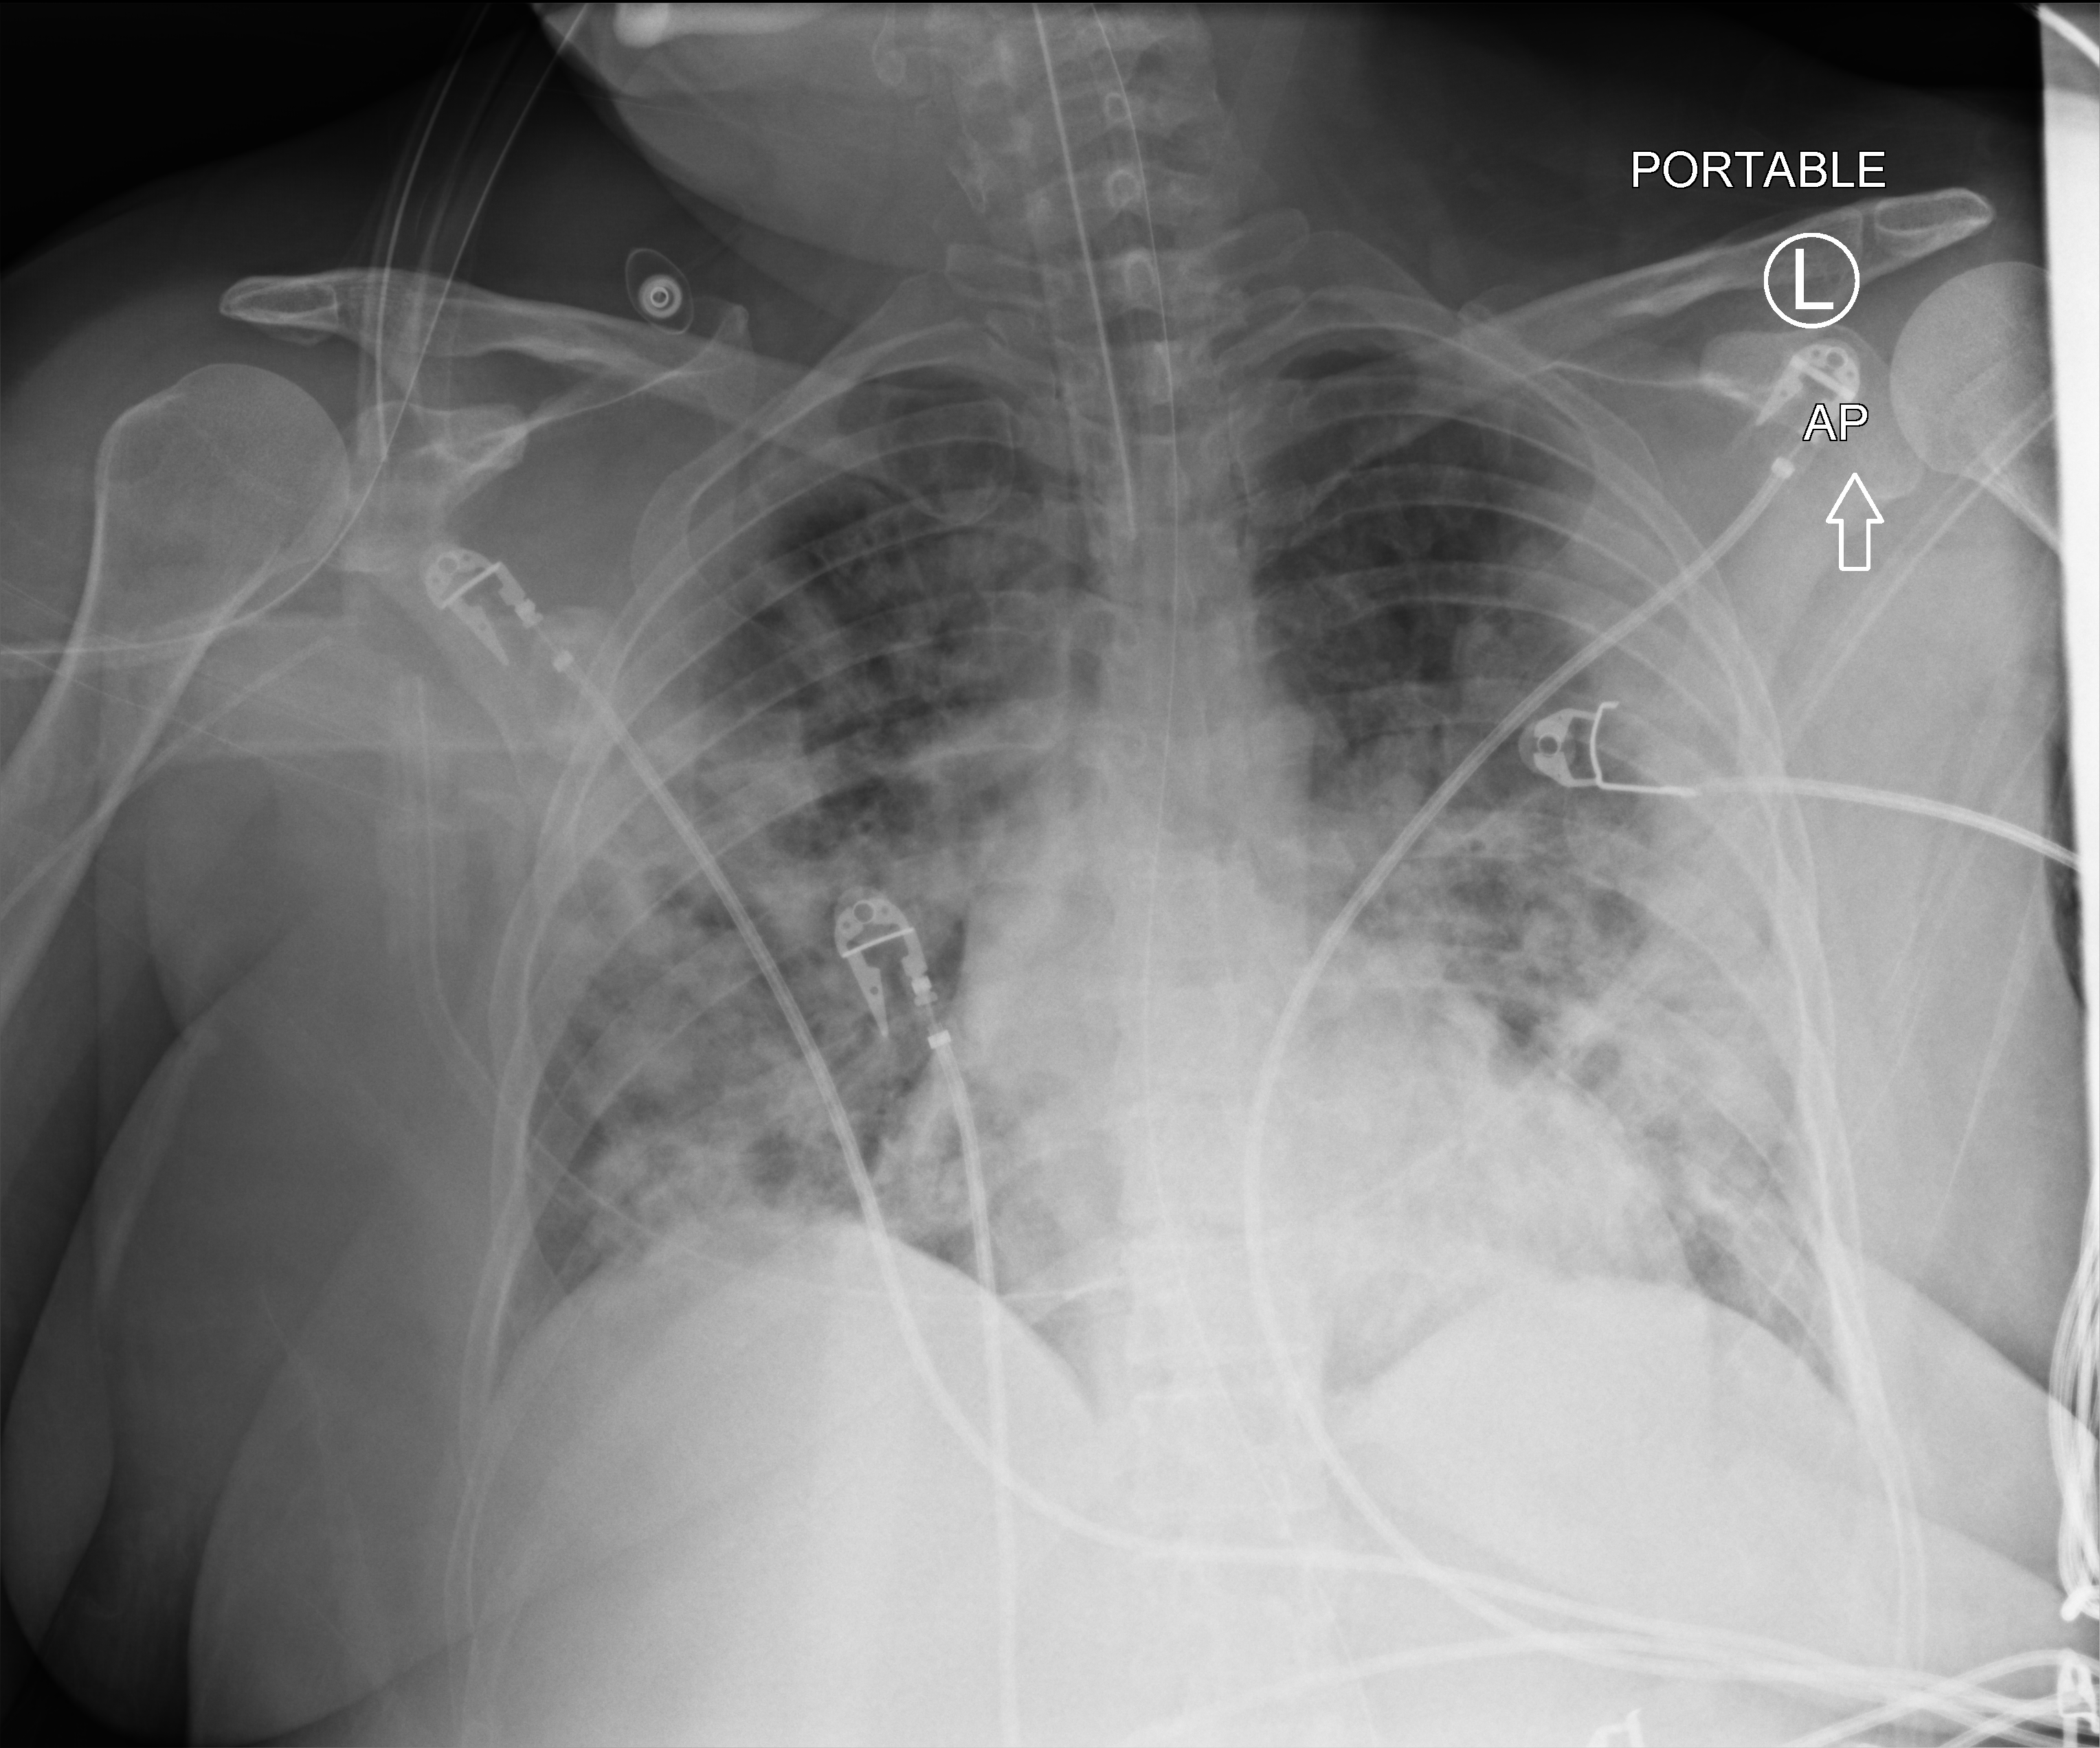
Portable chest radiograph. Patient hospitalised with COVID-19; female, aged 18–59 years.
From the hospital-stay record, not from the radiograph (when in the stay this image was taken is not recorded):
- length of hospital stay: 31 days